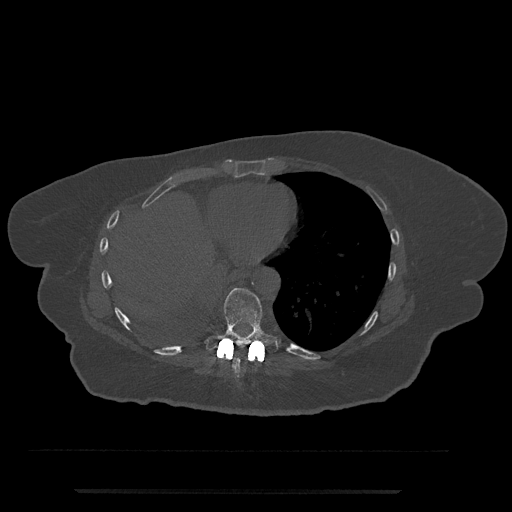
CT including the spine, one axial slice. Slice 345 of 797 in the series (ordered by position). Reconstruction kernel Br40s/3. Bone window (W 1800 / L 400 HU). 512 × 512 image matrix, field of view 440 × 440 mm. Patient: female, 51 years. Case-level facts recorded for this patient, not image findings: primary cancer: neuro.
Annotated regions visible in this slice (semi-automatic segmentation, software-assisted and operator-edited):
- T8 vertebra: bounding box <233,349,250,375> (left, top, right, bottom; pixels)
- T9 vertebra: <205,288,277,353>